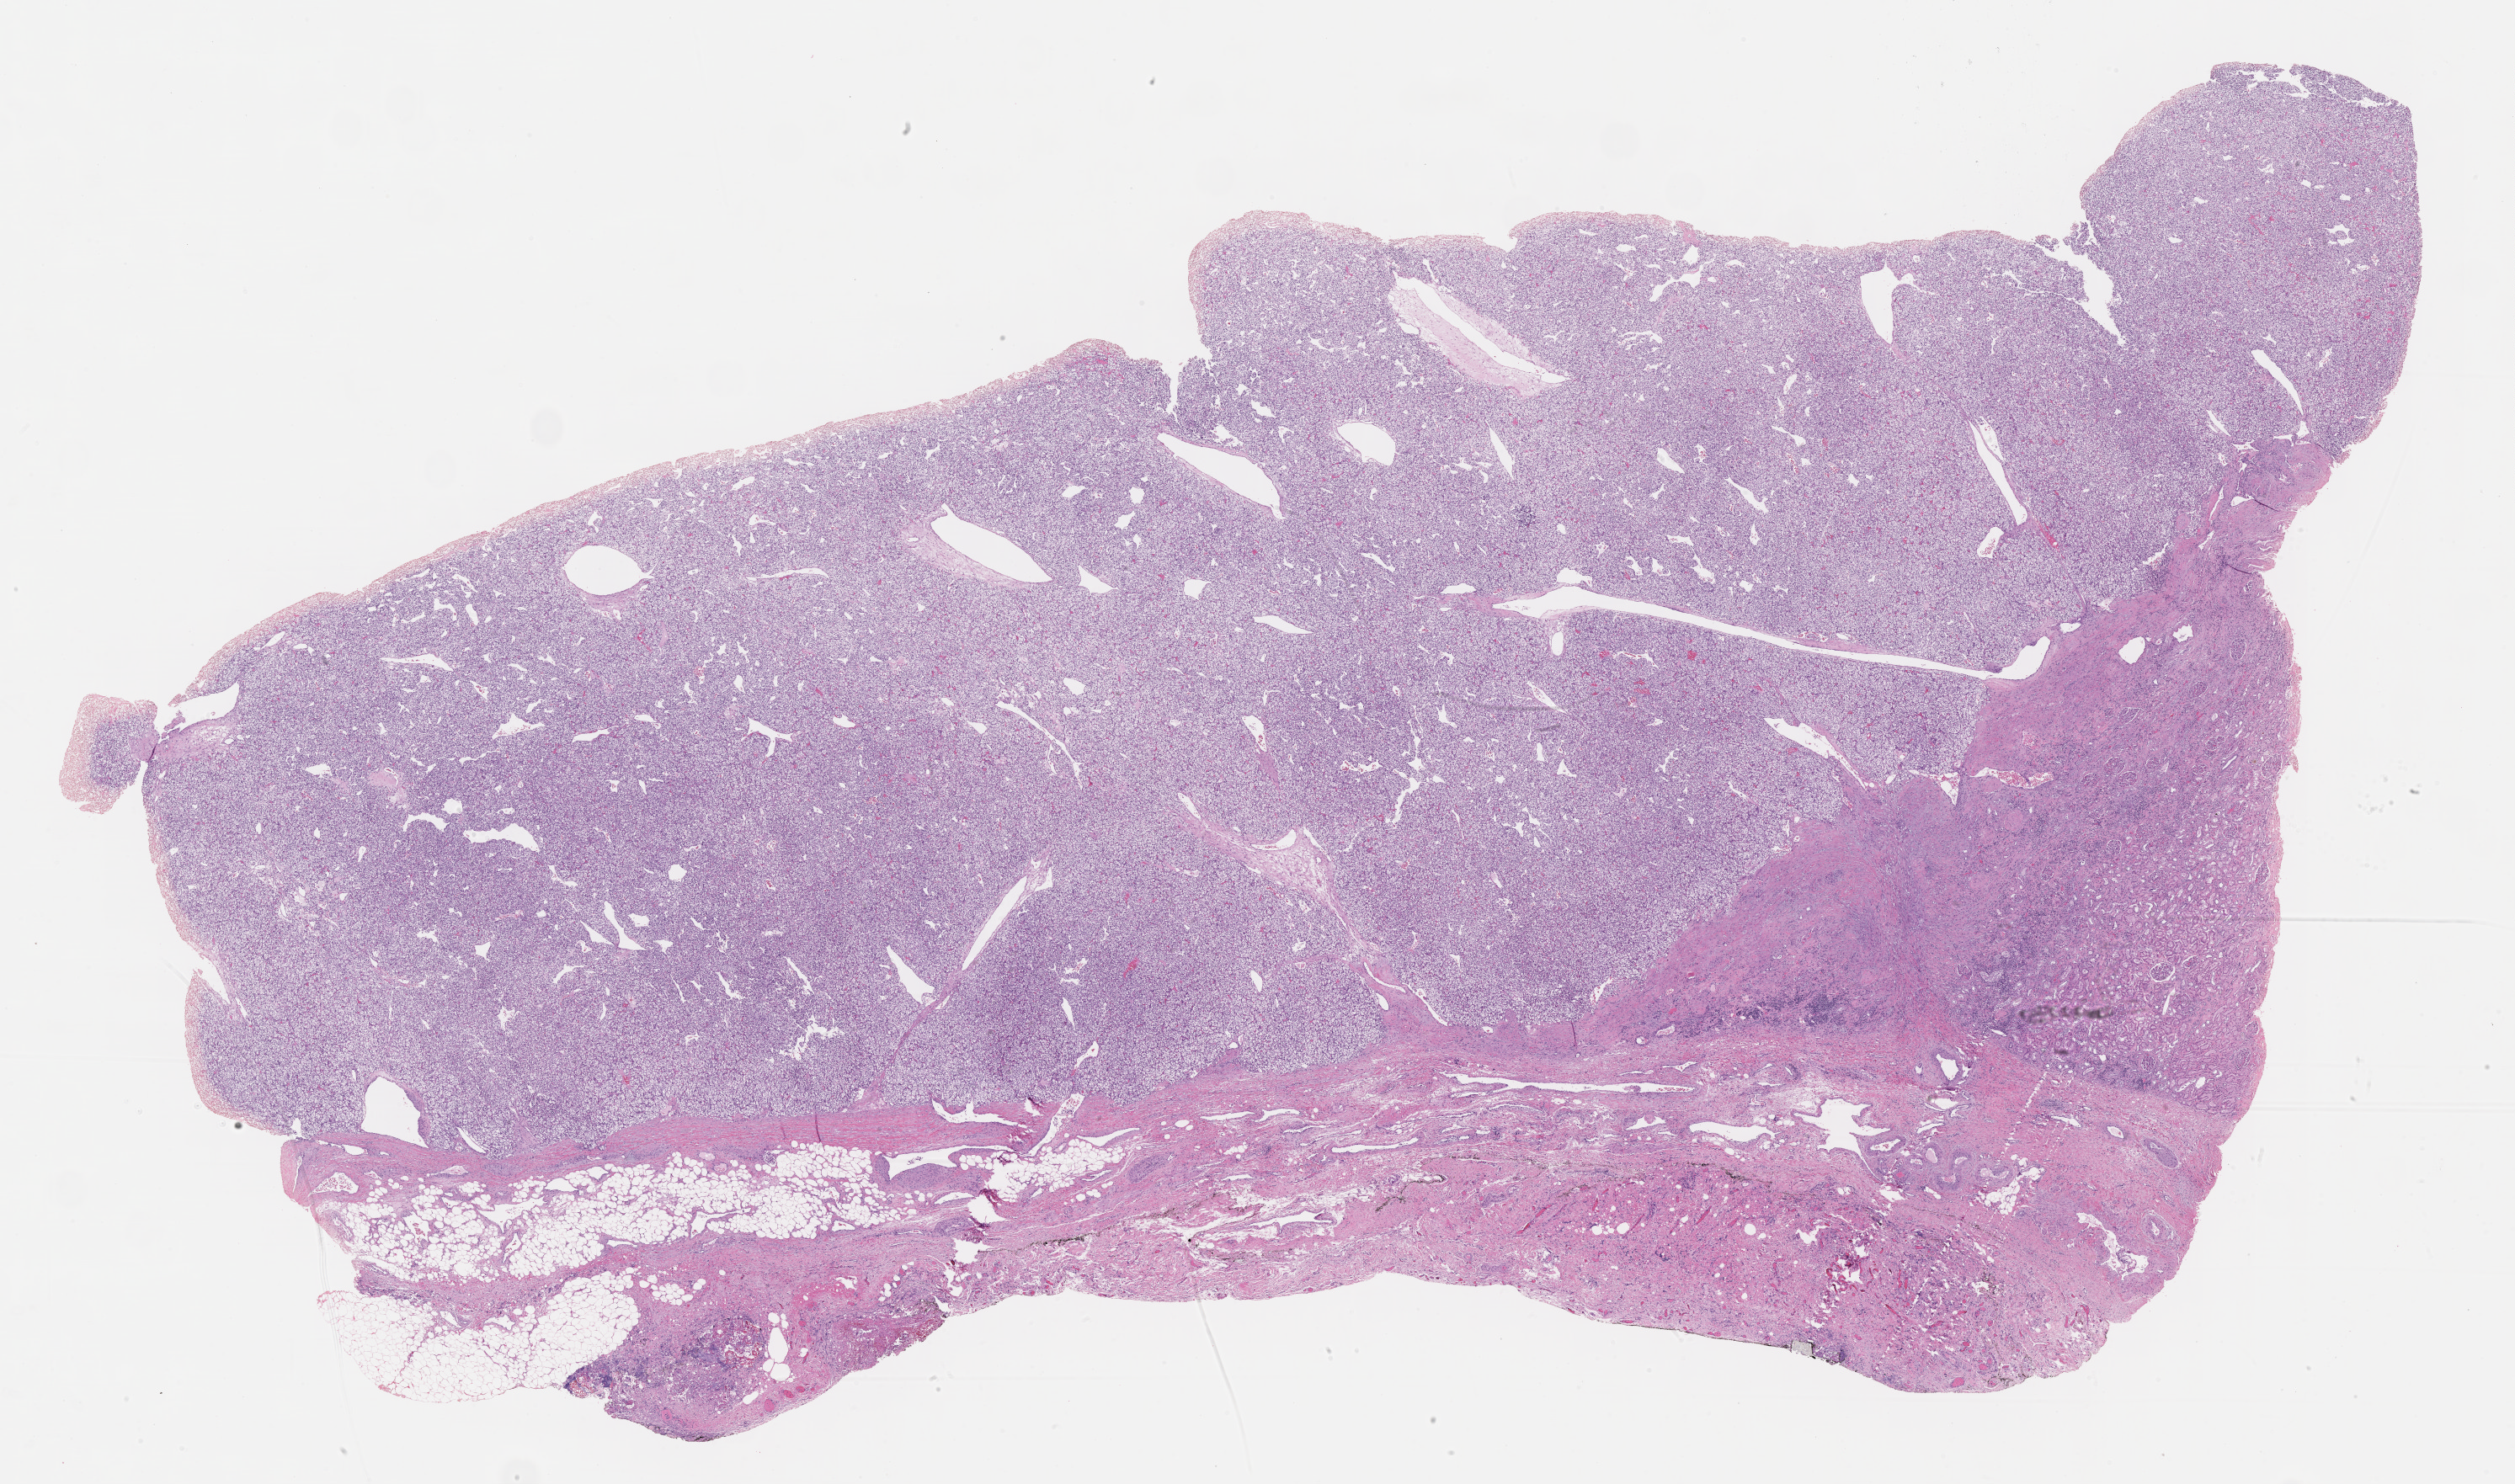
H&E-stained whole-slide image — shown as a low-resolution overview of the whole scanned area (about 24.2 x 14.3 mm). Formalin-fixed paraffin-embedded (FFPE) diagnostic section. Sample: primary tumour, kidney. Female, age 71 years at initial diagnosis.
Histologic diagnosis: Clear cell adenocarcinoma, NOS.